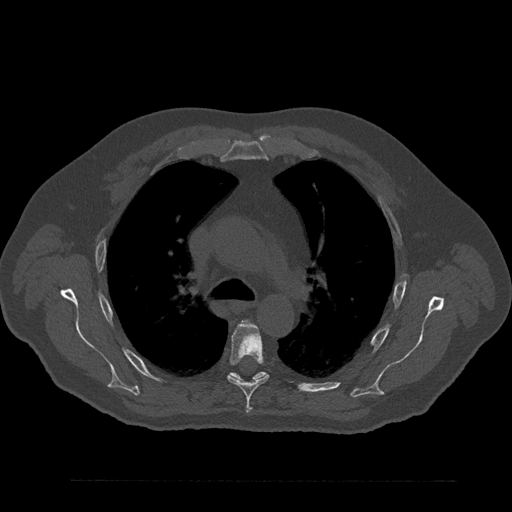
CT including the spine, one axial slice. Slice 595 of 797 in the series (ordered by position). Bone window (W 1800 / L 400 HU). 512 × 512 image matrix. Male patient, age 61 years. From the clinical record (not read from this slice): primary cancer: prostate.
Annotated regions visible in this slice (semi-automatic segmentation, software-assisted and operator-edited):
- T5 vertebra: box from (x=227, y=322) to (x=269, y=410) px
- T6 vertebra: (x=228, y=372)–(x=267, y=382)